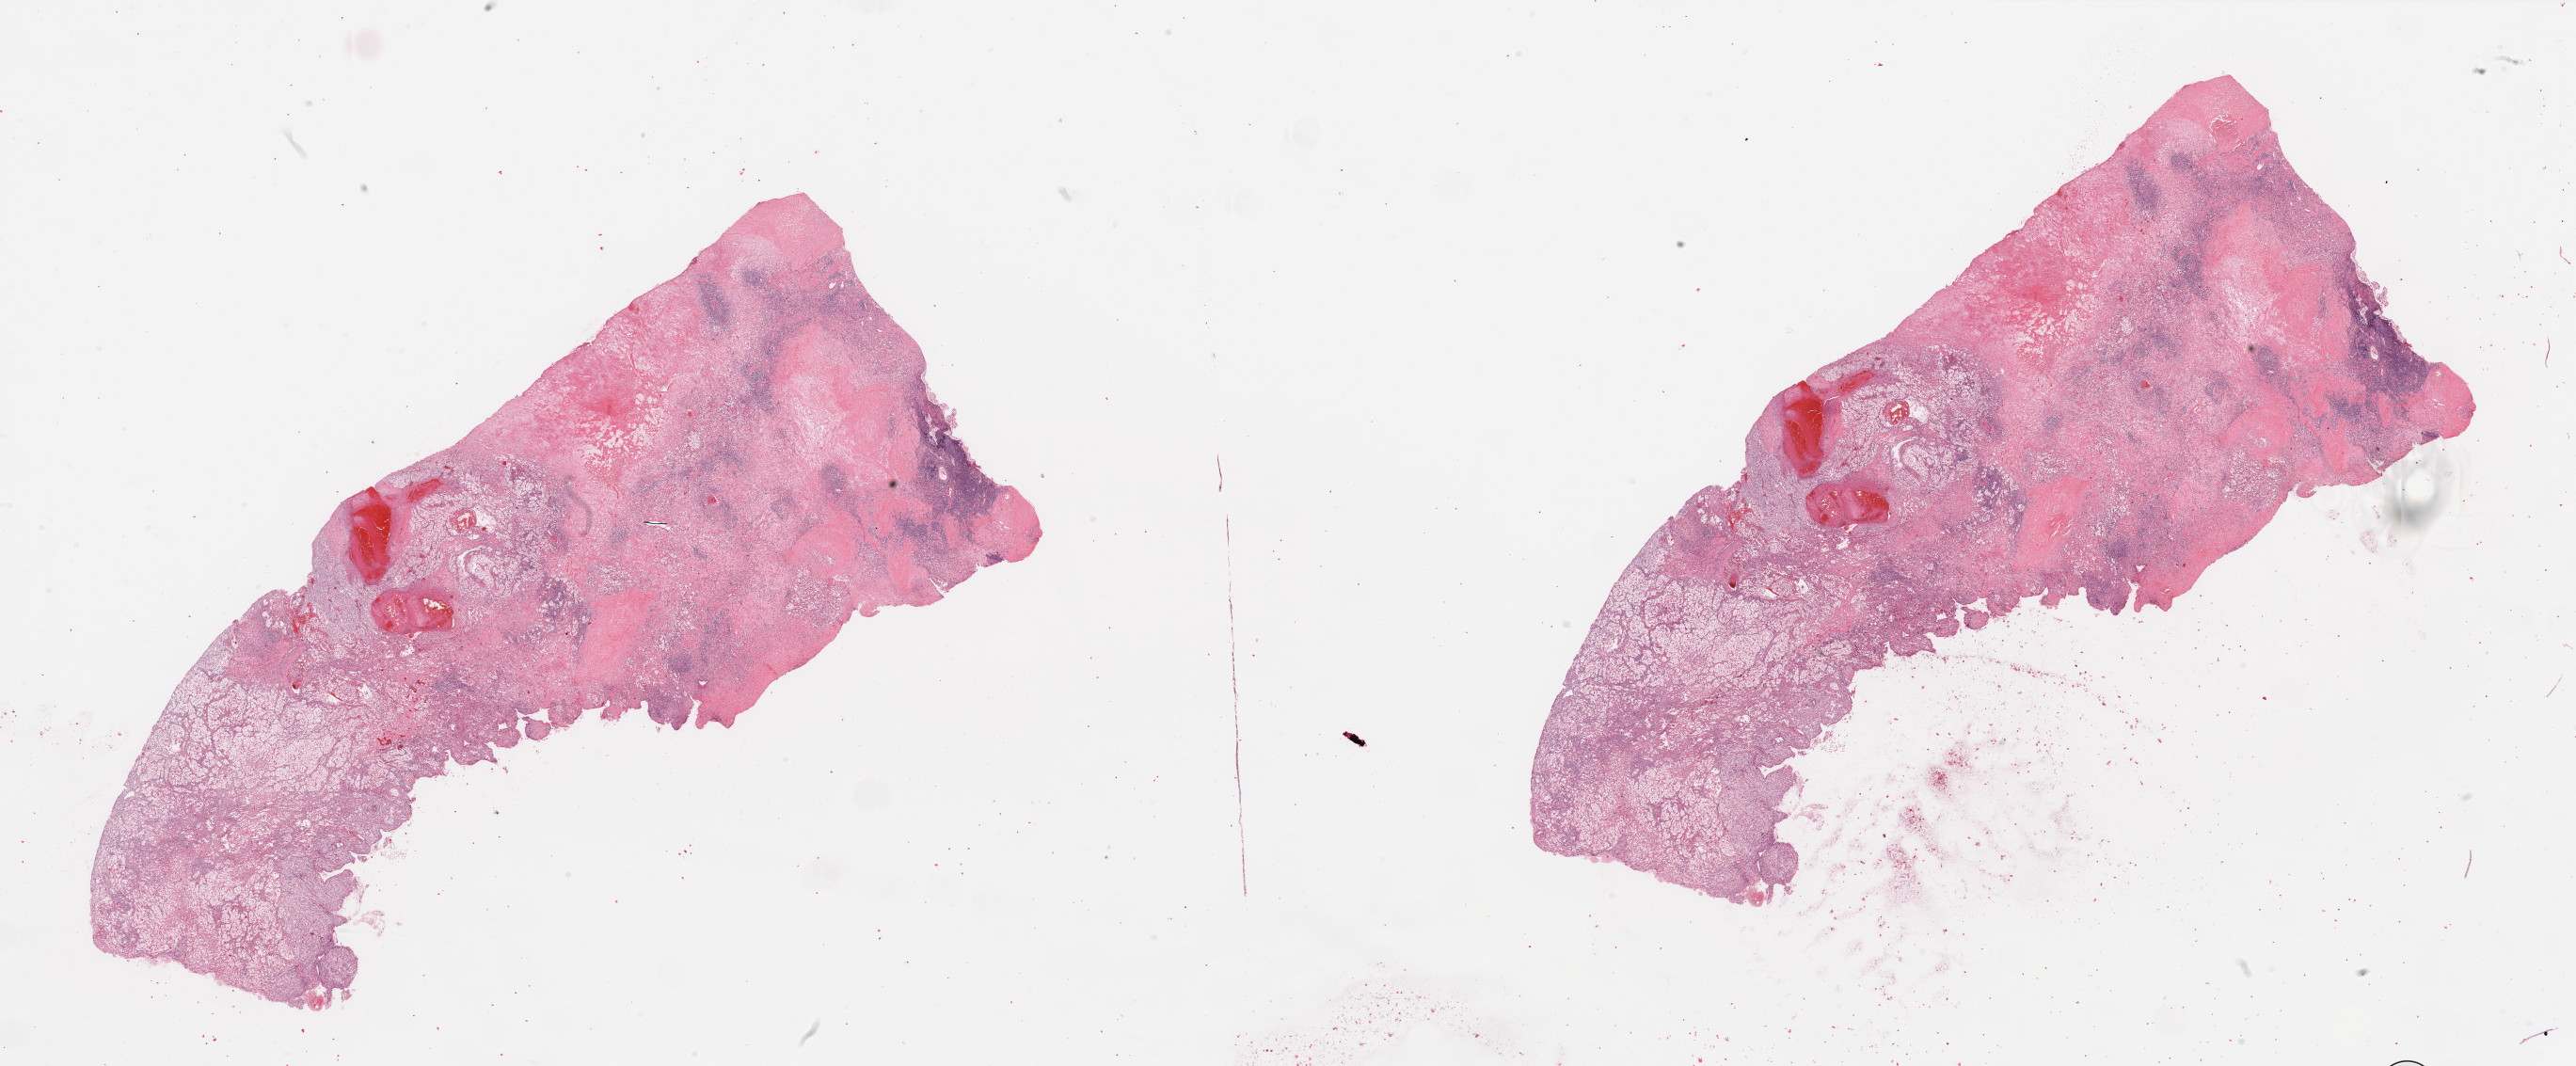
Whole-slide histology image, Hematoxylin and eosin (H&E) stained, shown as a low-resolution overview of the whole scanned area (about 43.3 x 17.9 mm, slide scanned at 20x); kidney, tumour tissue. 66-year-old female patient.
Histologic diagnosis: Renal cell carcinoma, NOS.